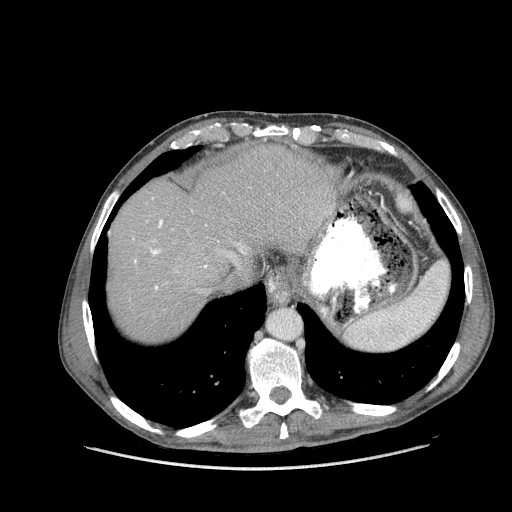
Contrast-enhanced abdominal CT (liver protocol), one axial slice; slice 127 of 162 in the series (ordered by position); reconstruction kernel STANDARD; 100 kVp; soft-tissue window (W 400 / L 40 HU); 2.5 mm slice thickness; 512 × 512 image matrix, field of view 400 × 400 mm. Case-level facts recorded for this patient, not image findings: diagnosis: hepatocellular carcinoma (patient treated with transarterial chemoembolisation; whether this scan precedes or follows treatment is not stated here); TNM stage (as recorded): Stage-IIIA; Child-Pugh class: A; tumour nodularity: multinodular; tumour size: 9.9 cm.
Structures marked on this image (semi-automatic segmentation, software-assisted and operator-edited):
- abdominal aorta: box from (x=270, y=310) to (x=301, y=340) px
- liver parenchyma outside the tumour (the mass and vessels are separate outlines, so this box may not span the whole liver): (x=108, y=144)–(x=336, y=340)
- liver vessels: (x=134, y=220)–(x=245, y=290)